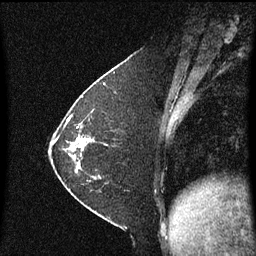
Breast MRI (dynamic contrast-enhanced), one sagittal slice; slice 22 of 60 in the series (ordered by position); dynamic contrast-enhanced series, image 2 of 3 at this slice position (ordered by acquisition); 1.5 T; TE 4.2 ms, TR 8.4 ms; 2 mm slice thickness; 256 × 256 image matrix, field of view 200 × 200 mm. Patient: female, 36 years. Case-level facts recorded for this patient, not image findings: setting: breast cancer imaged before/during neoadjuvant chemotherapy; receptor status: HR-positive, HER2-negative.
Structures marked on this image (semi-automatic segmentation, software-assisted and operator-edited):
- analysis volume of interest (the breast-tissue region the enhancement analysis was run in; not a lesion): bounding box (x1, y1, x2, y2) in pixels: (72, 118, 117, 181)
- tumour enhancement mask (voxels above the 70 % enhancement threshold inside the analysis volume of interest): (72, 136, 93, 153)